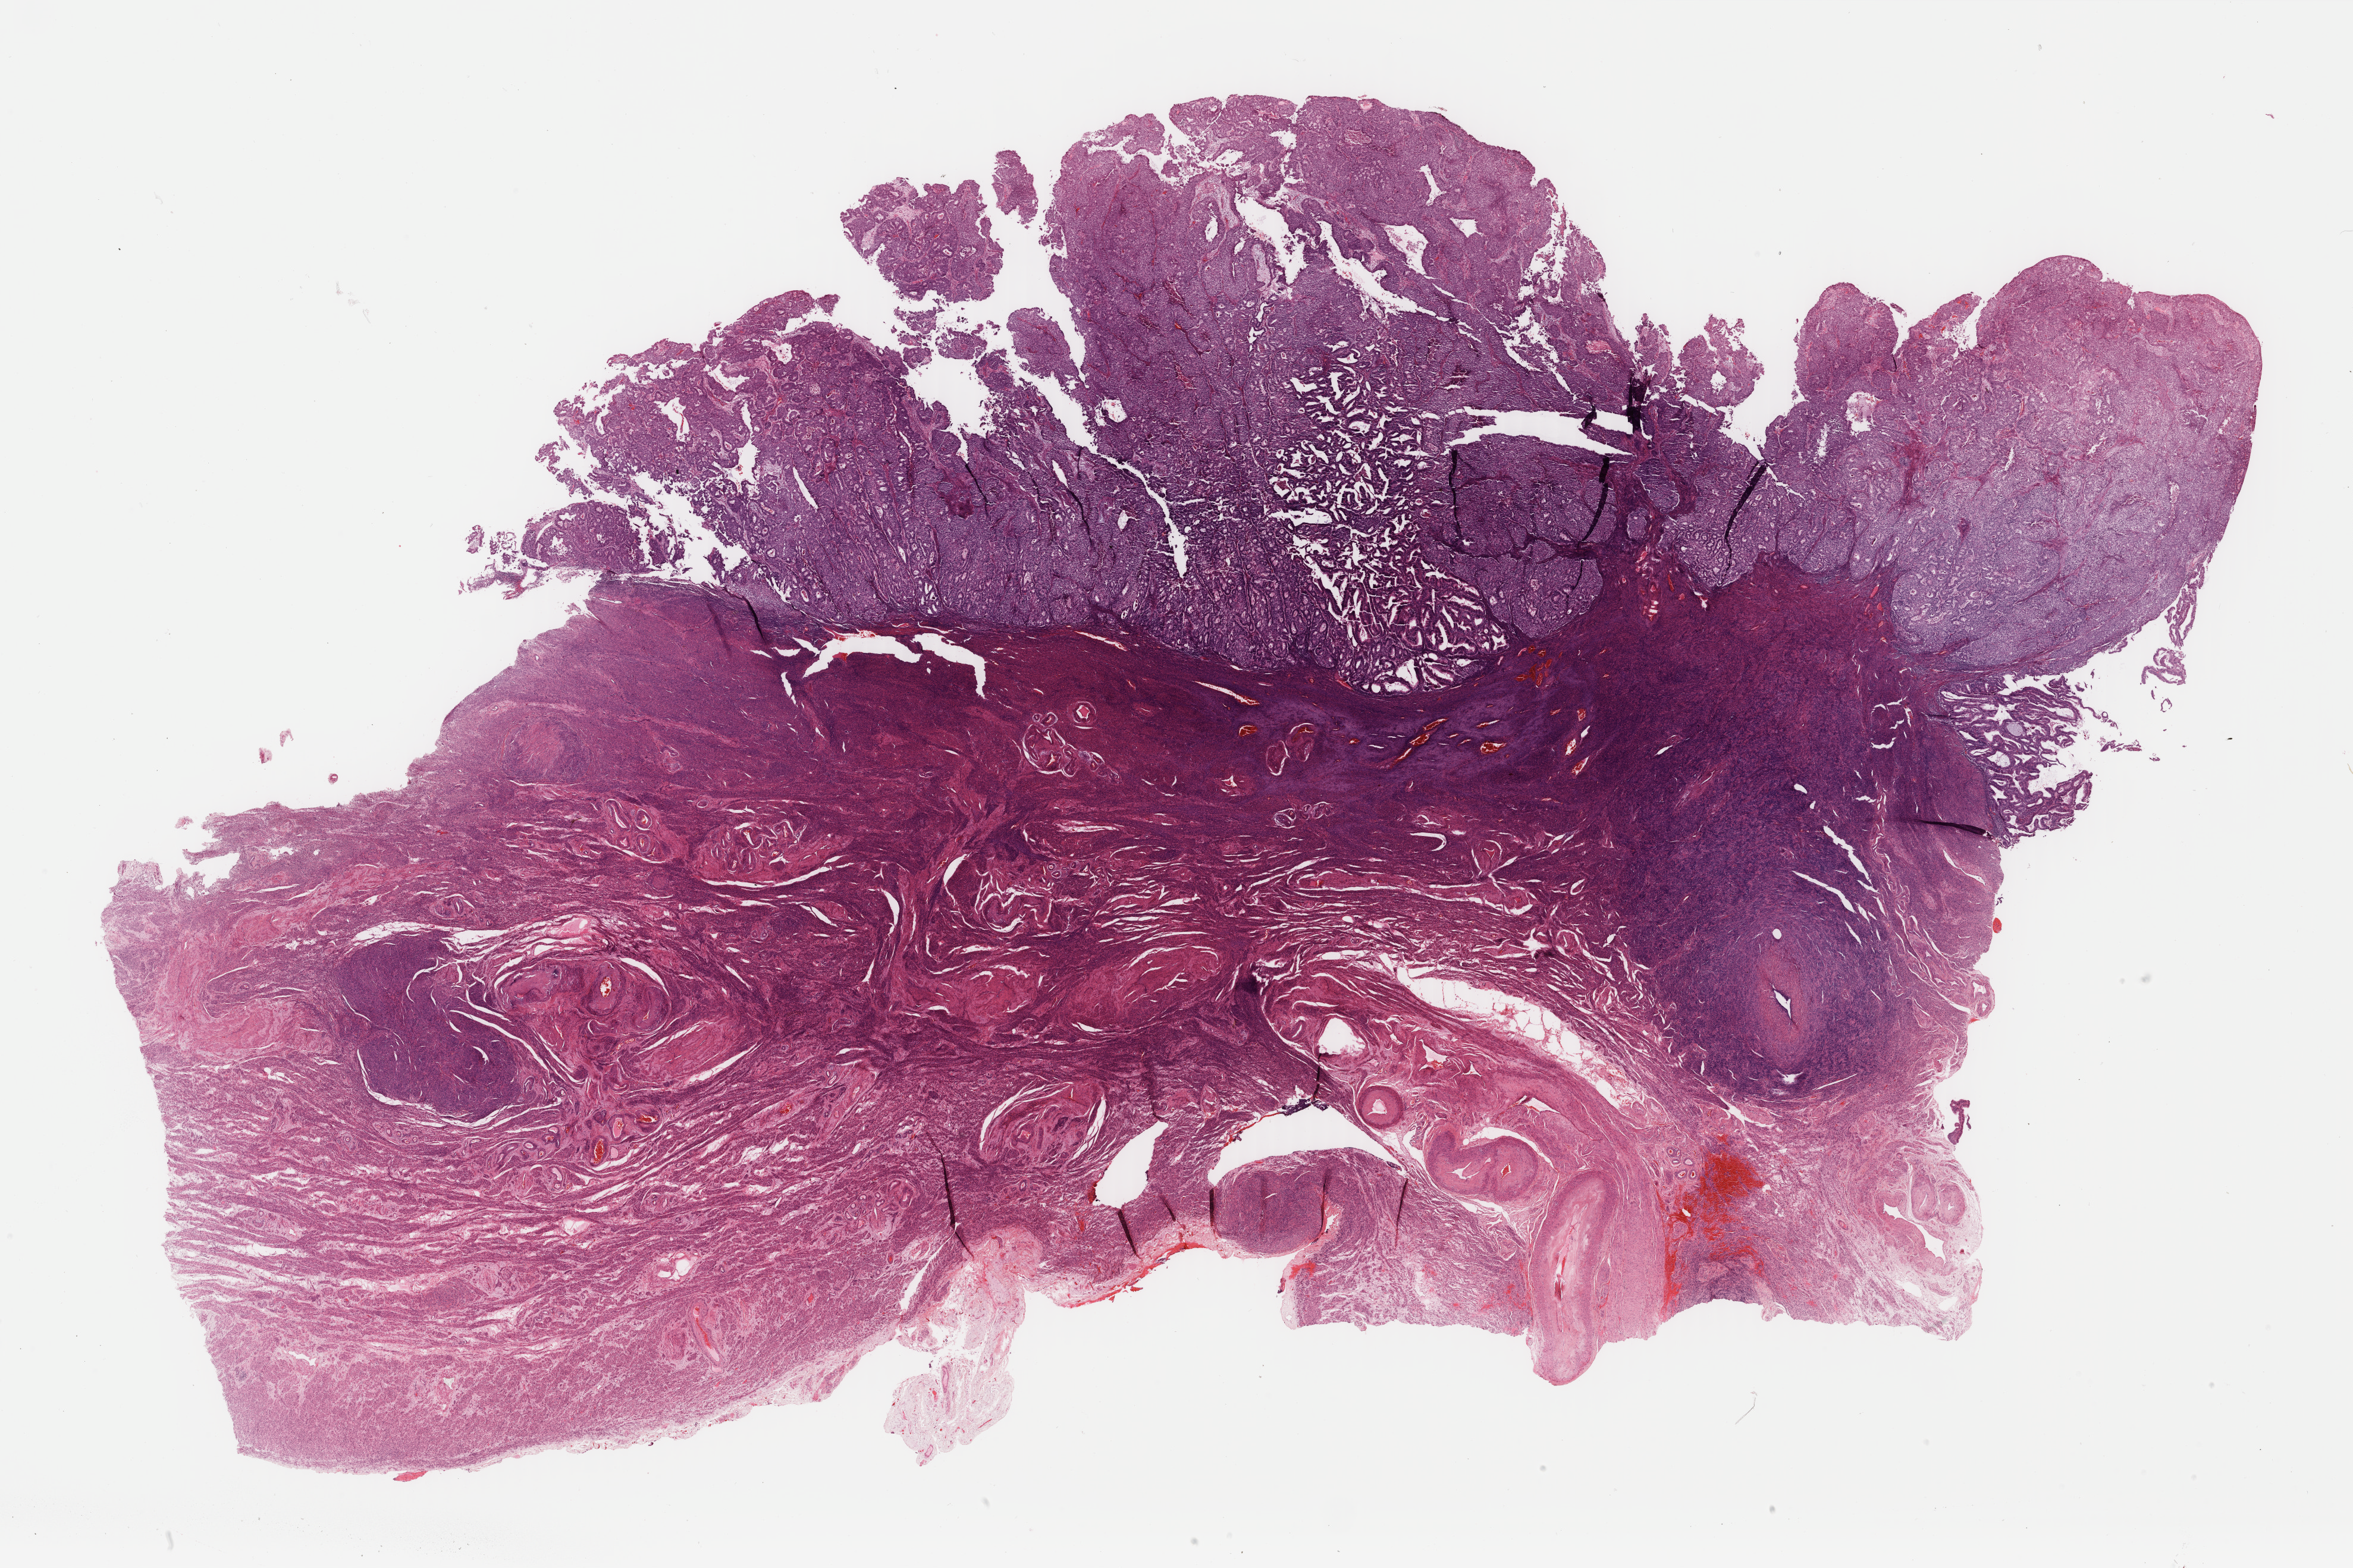
H&E whole-slide image — a low-resolution overview of the entire scanned area, about 31.4 x 20.9 mm (slide scanned at 40x). Formalin-fixed paraffin-embedded (FFPE) diagnostic section. Primary tumour sample from the uterus. Female patient; age at initial diagnosis 76 years. Histologic grade: G1 (well differentiated).
FIGO stage: IA. Diagnosis: Endometrioid adenocarcinoma, NOS (endometrium).